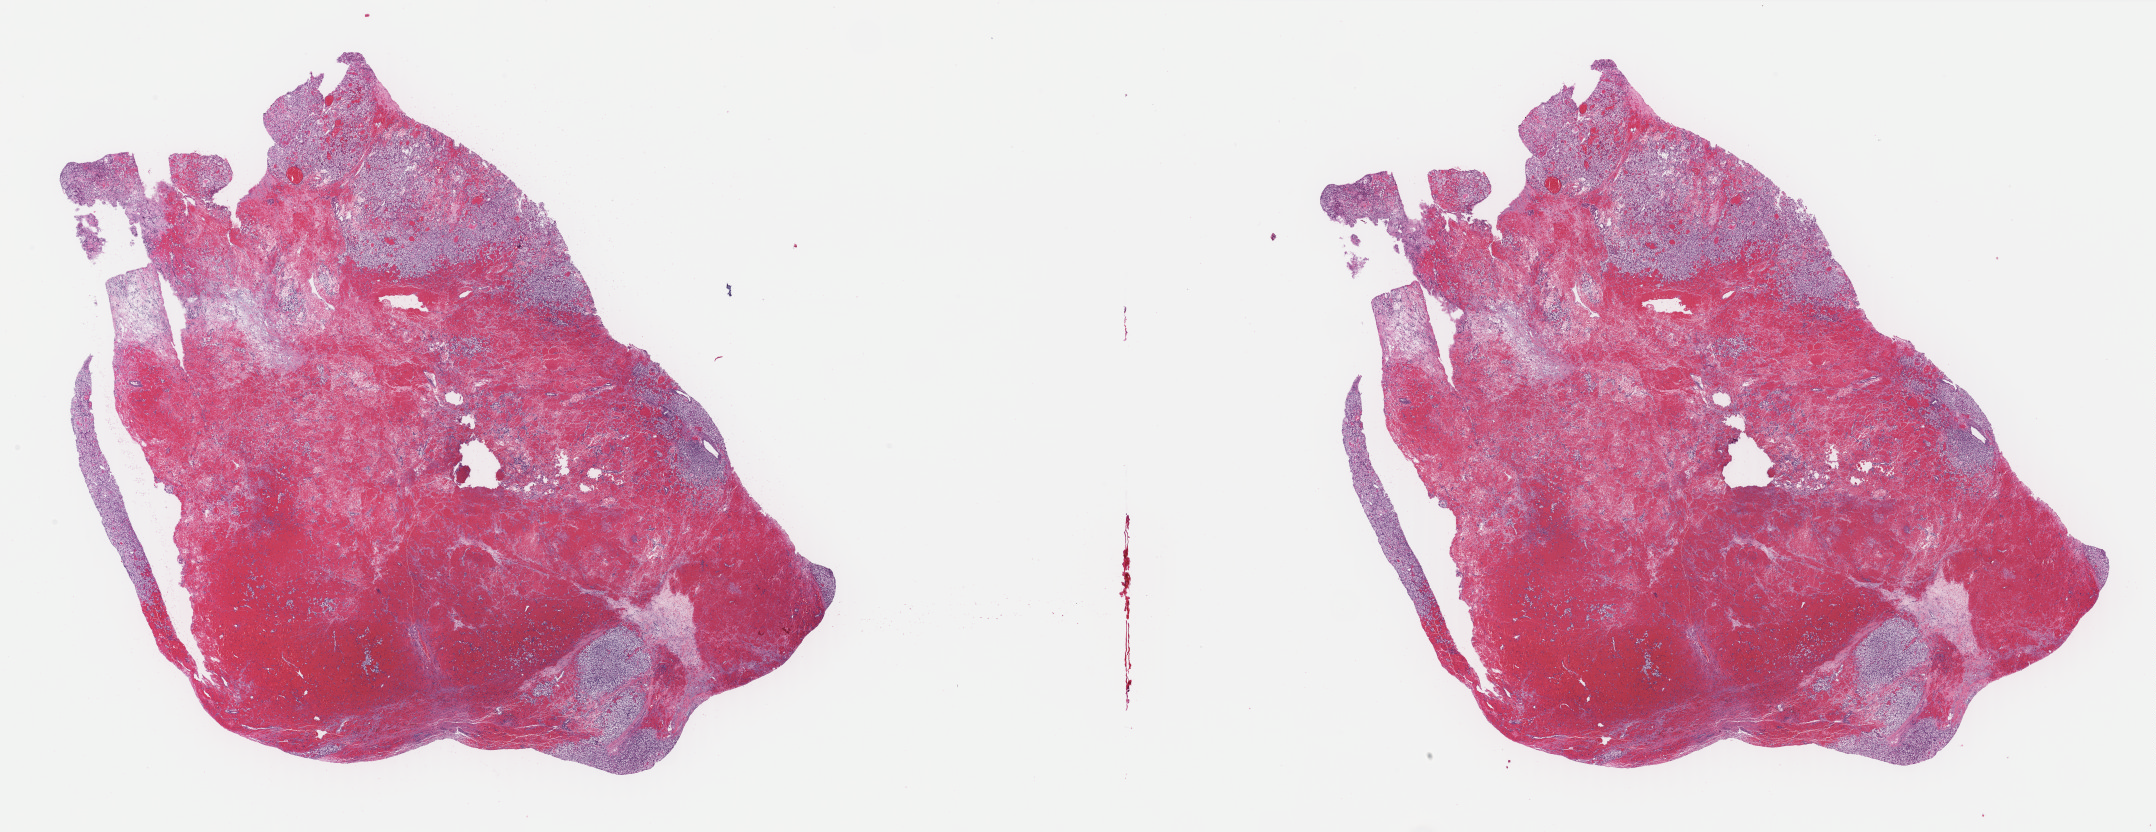
Digitized H&E-stained tissue section (whole slide) — a low-resolution overview of the entire scanned area, about 34.1 x 13.2 mm (acquisition: 40x scan); FFPE section; kidney, primary tumour sample. Patient: female, age at initial diagnosis 54 years. Histologic grade: G3 (poorly differentiated).
AJCC pathologic stage: I. Pathologic diagnosis: Clear cell adenocarcinoma, NOS. Laterality: left.